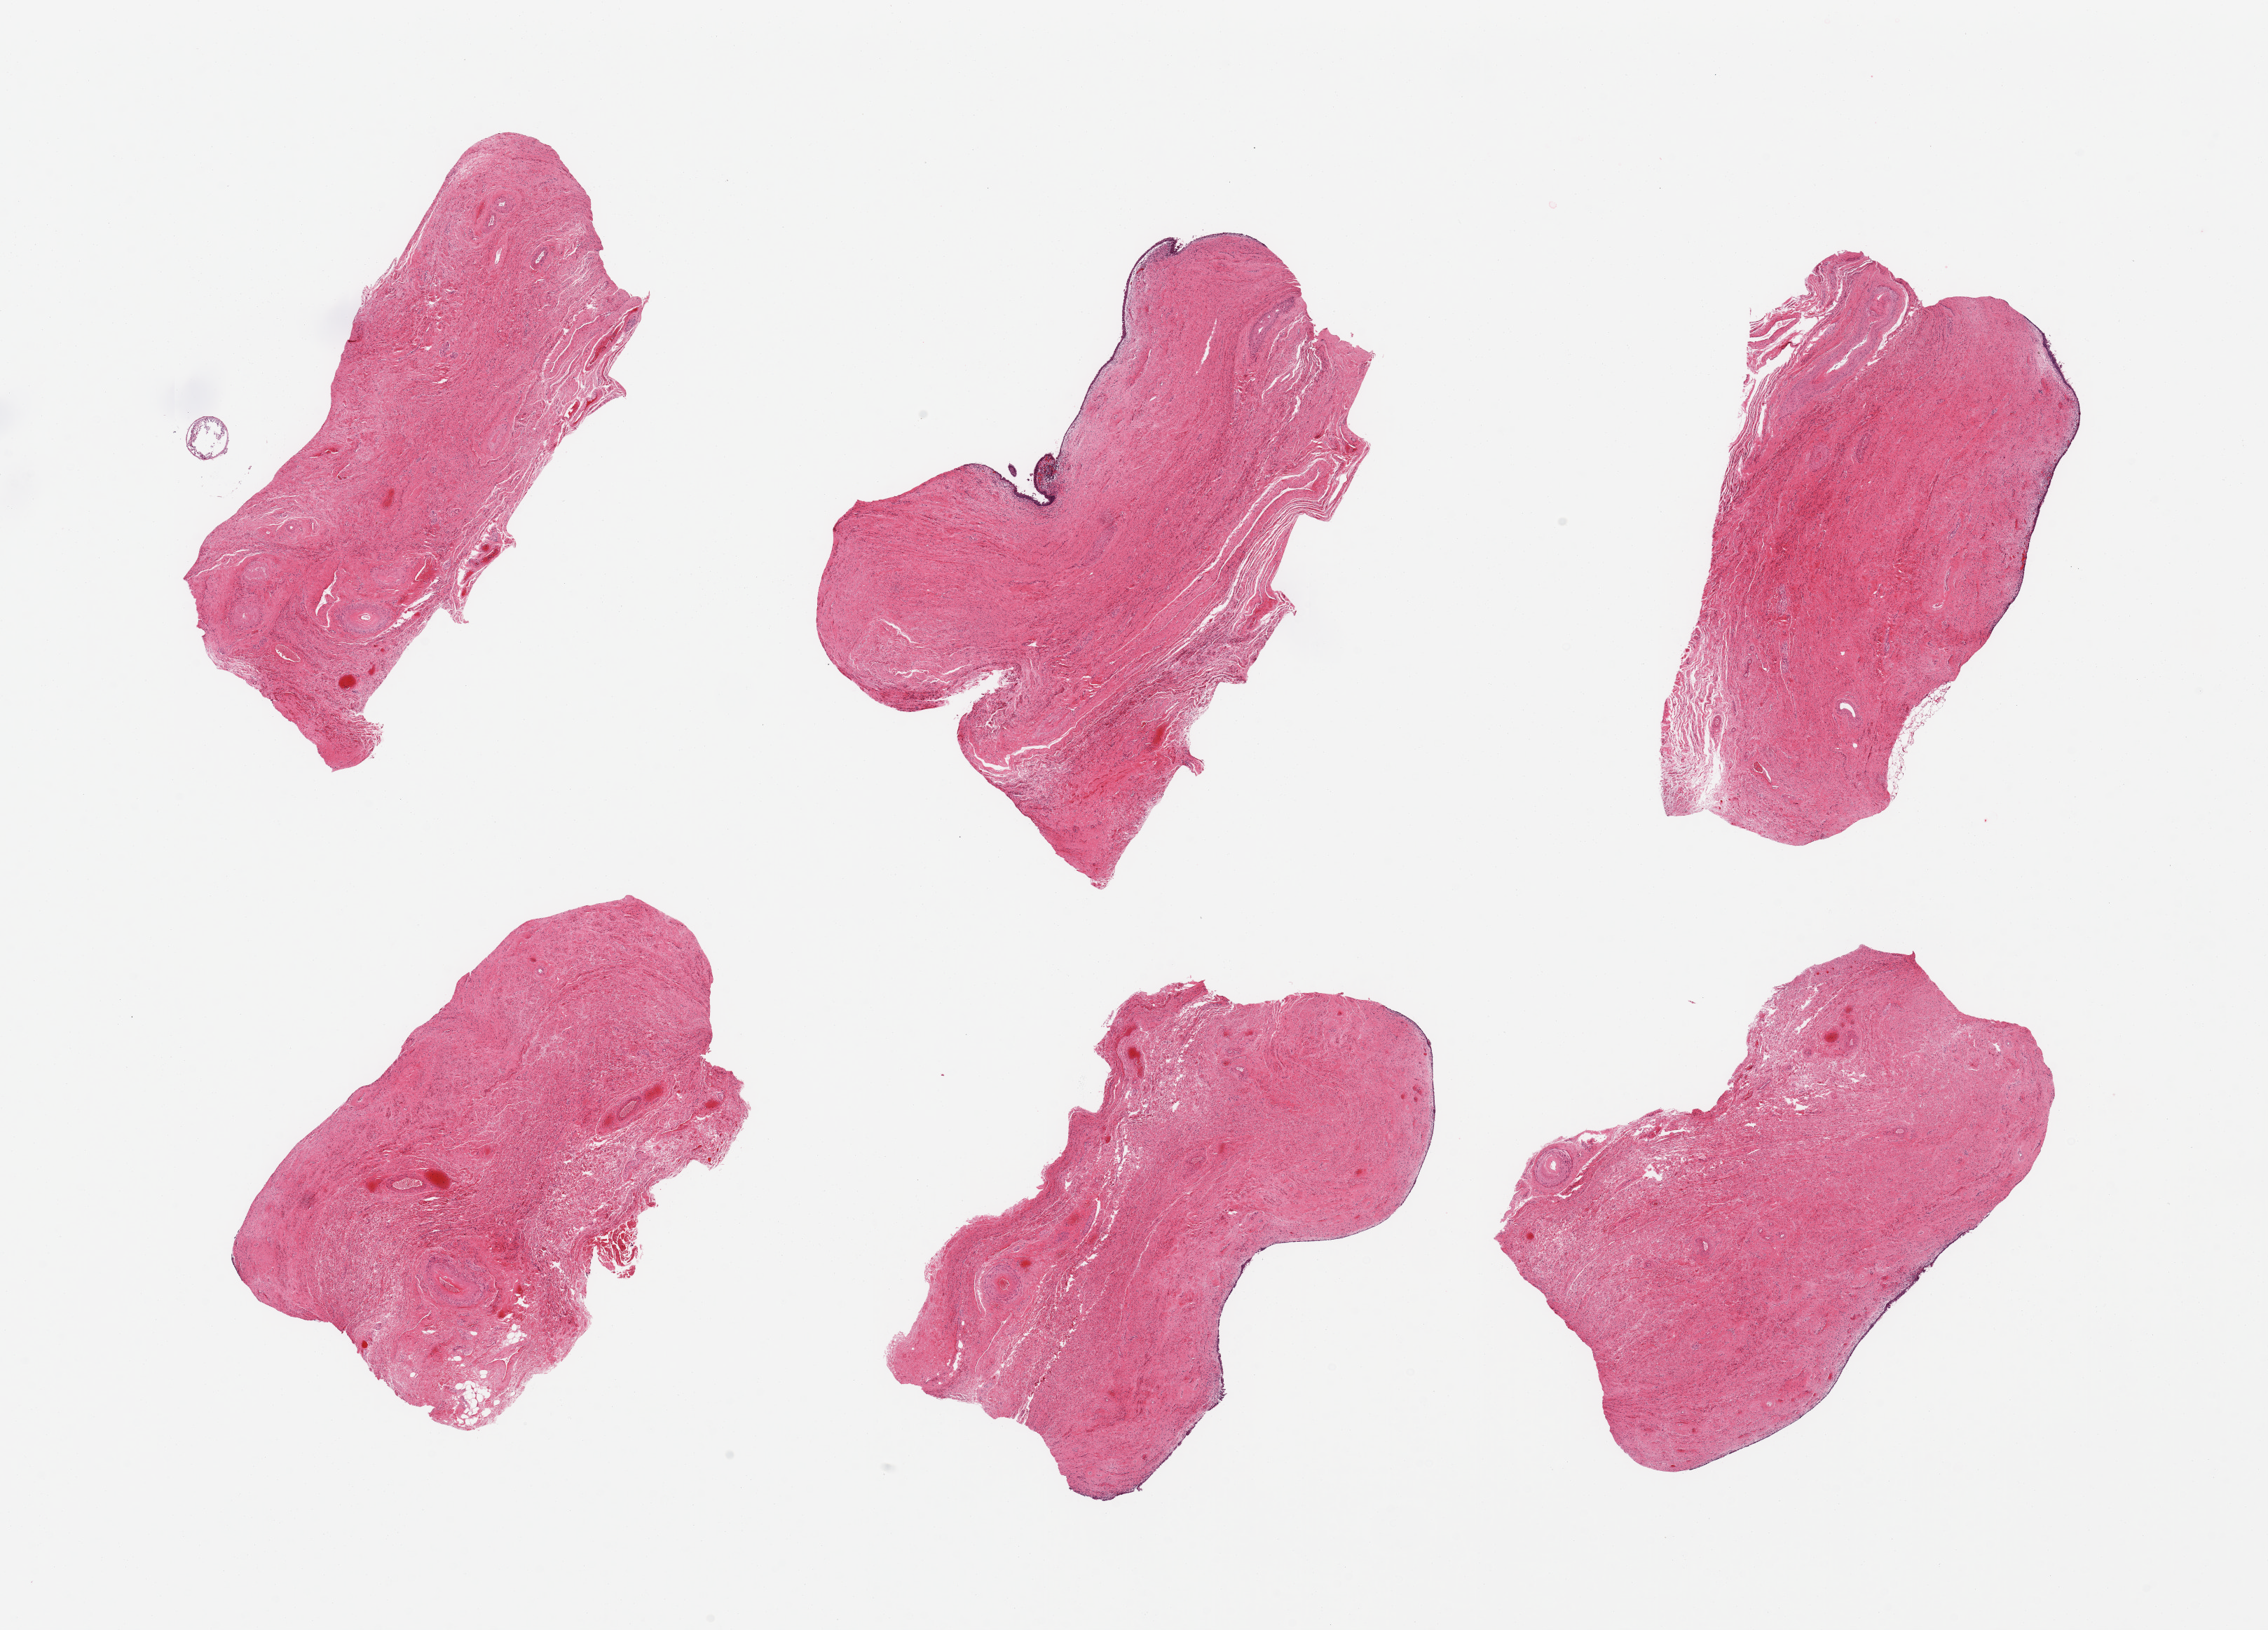
Haematoxylin and eosin whole-slide image, brightfield — whole scanned area (about 25.6 x 18.4 mm) shown as a low-resolution overview, PAXgene-fixed, paraffin-embedded tissue, target tissue: vagina, donor tissue sample.
- reviewer comment on this tissue sample: 6 pieces, mainly stroma; surface layers of mucosa largely sloughed